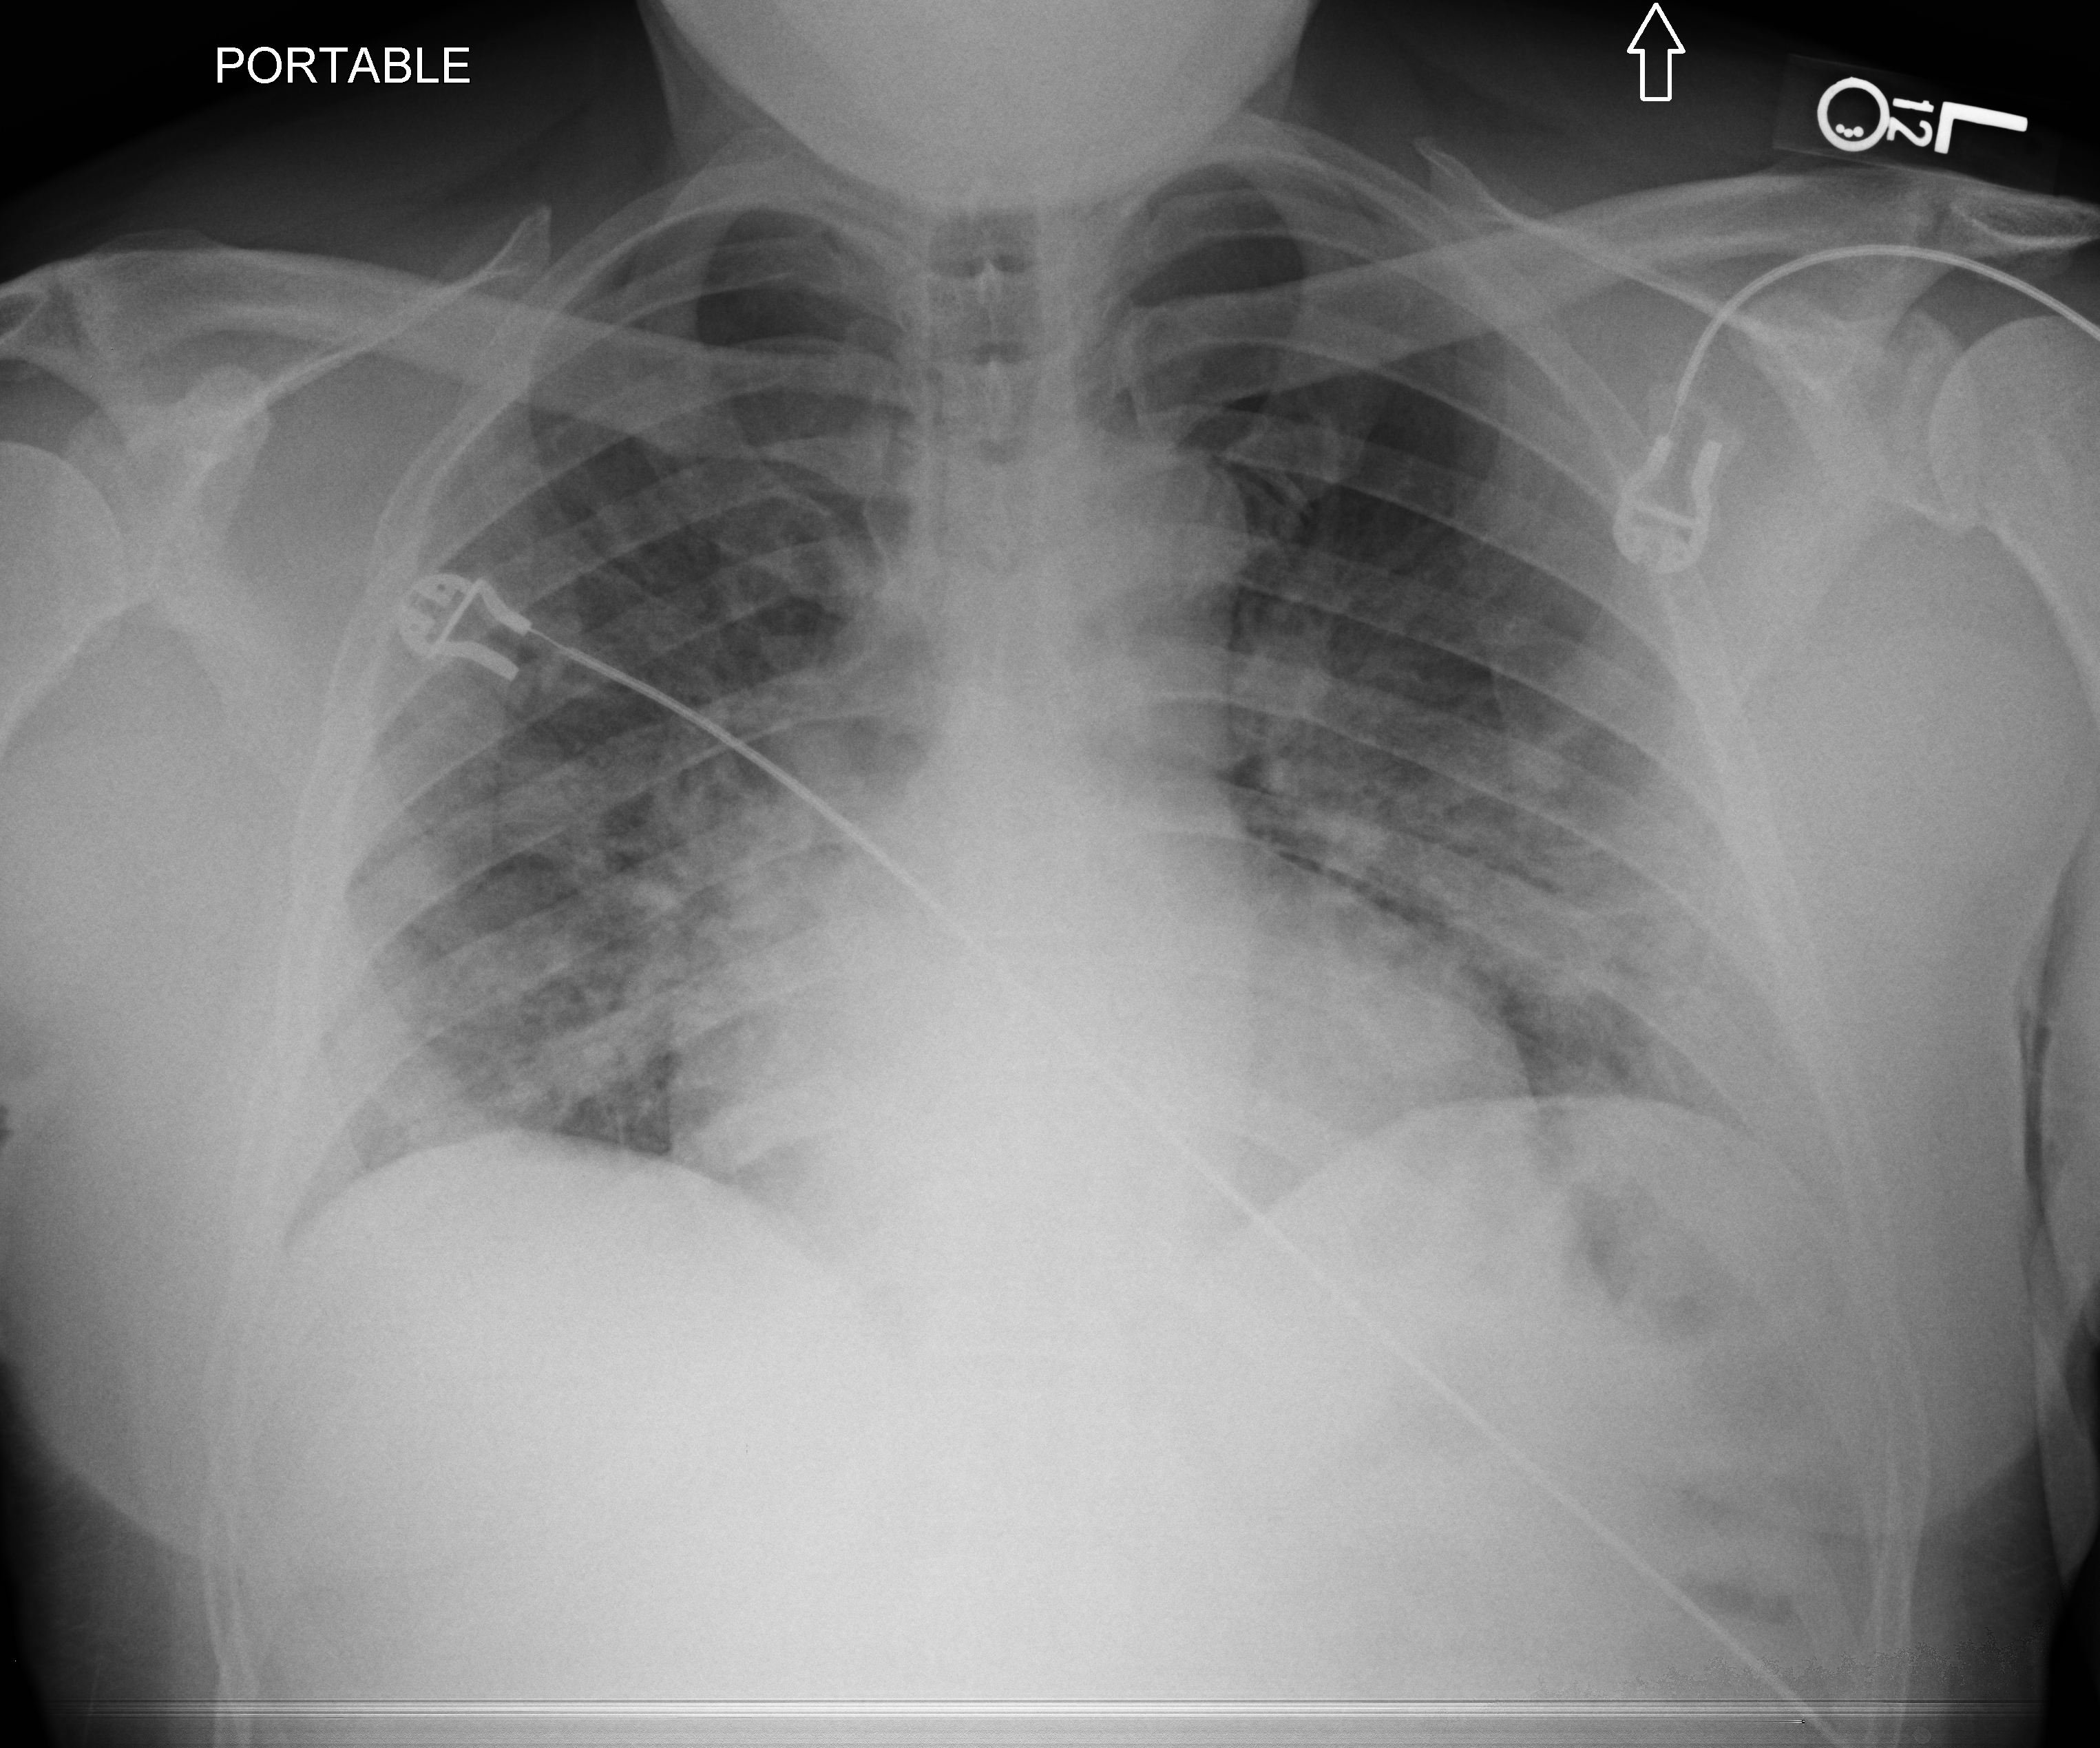
Bedside chest radiograph (computed radiography); anteroposterior (AP) projection. Male patient hospitalised with COVID-19, age 18–59 years.
Admission-level facts for this patient (not findings on this image; timing relative to this image not recorded): smoking status (admission record): former; admitted to intensive care during this hospital stay: no.